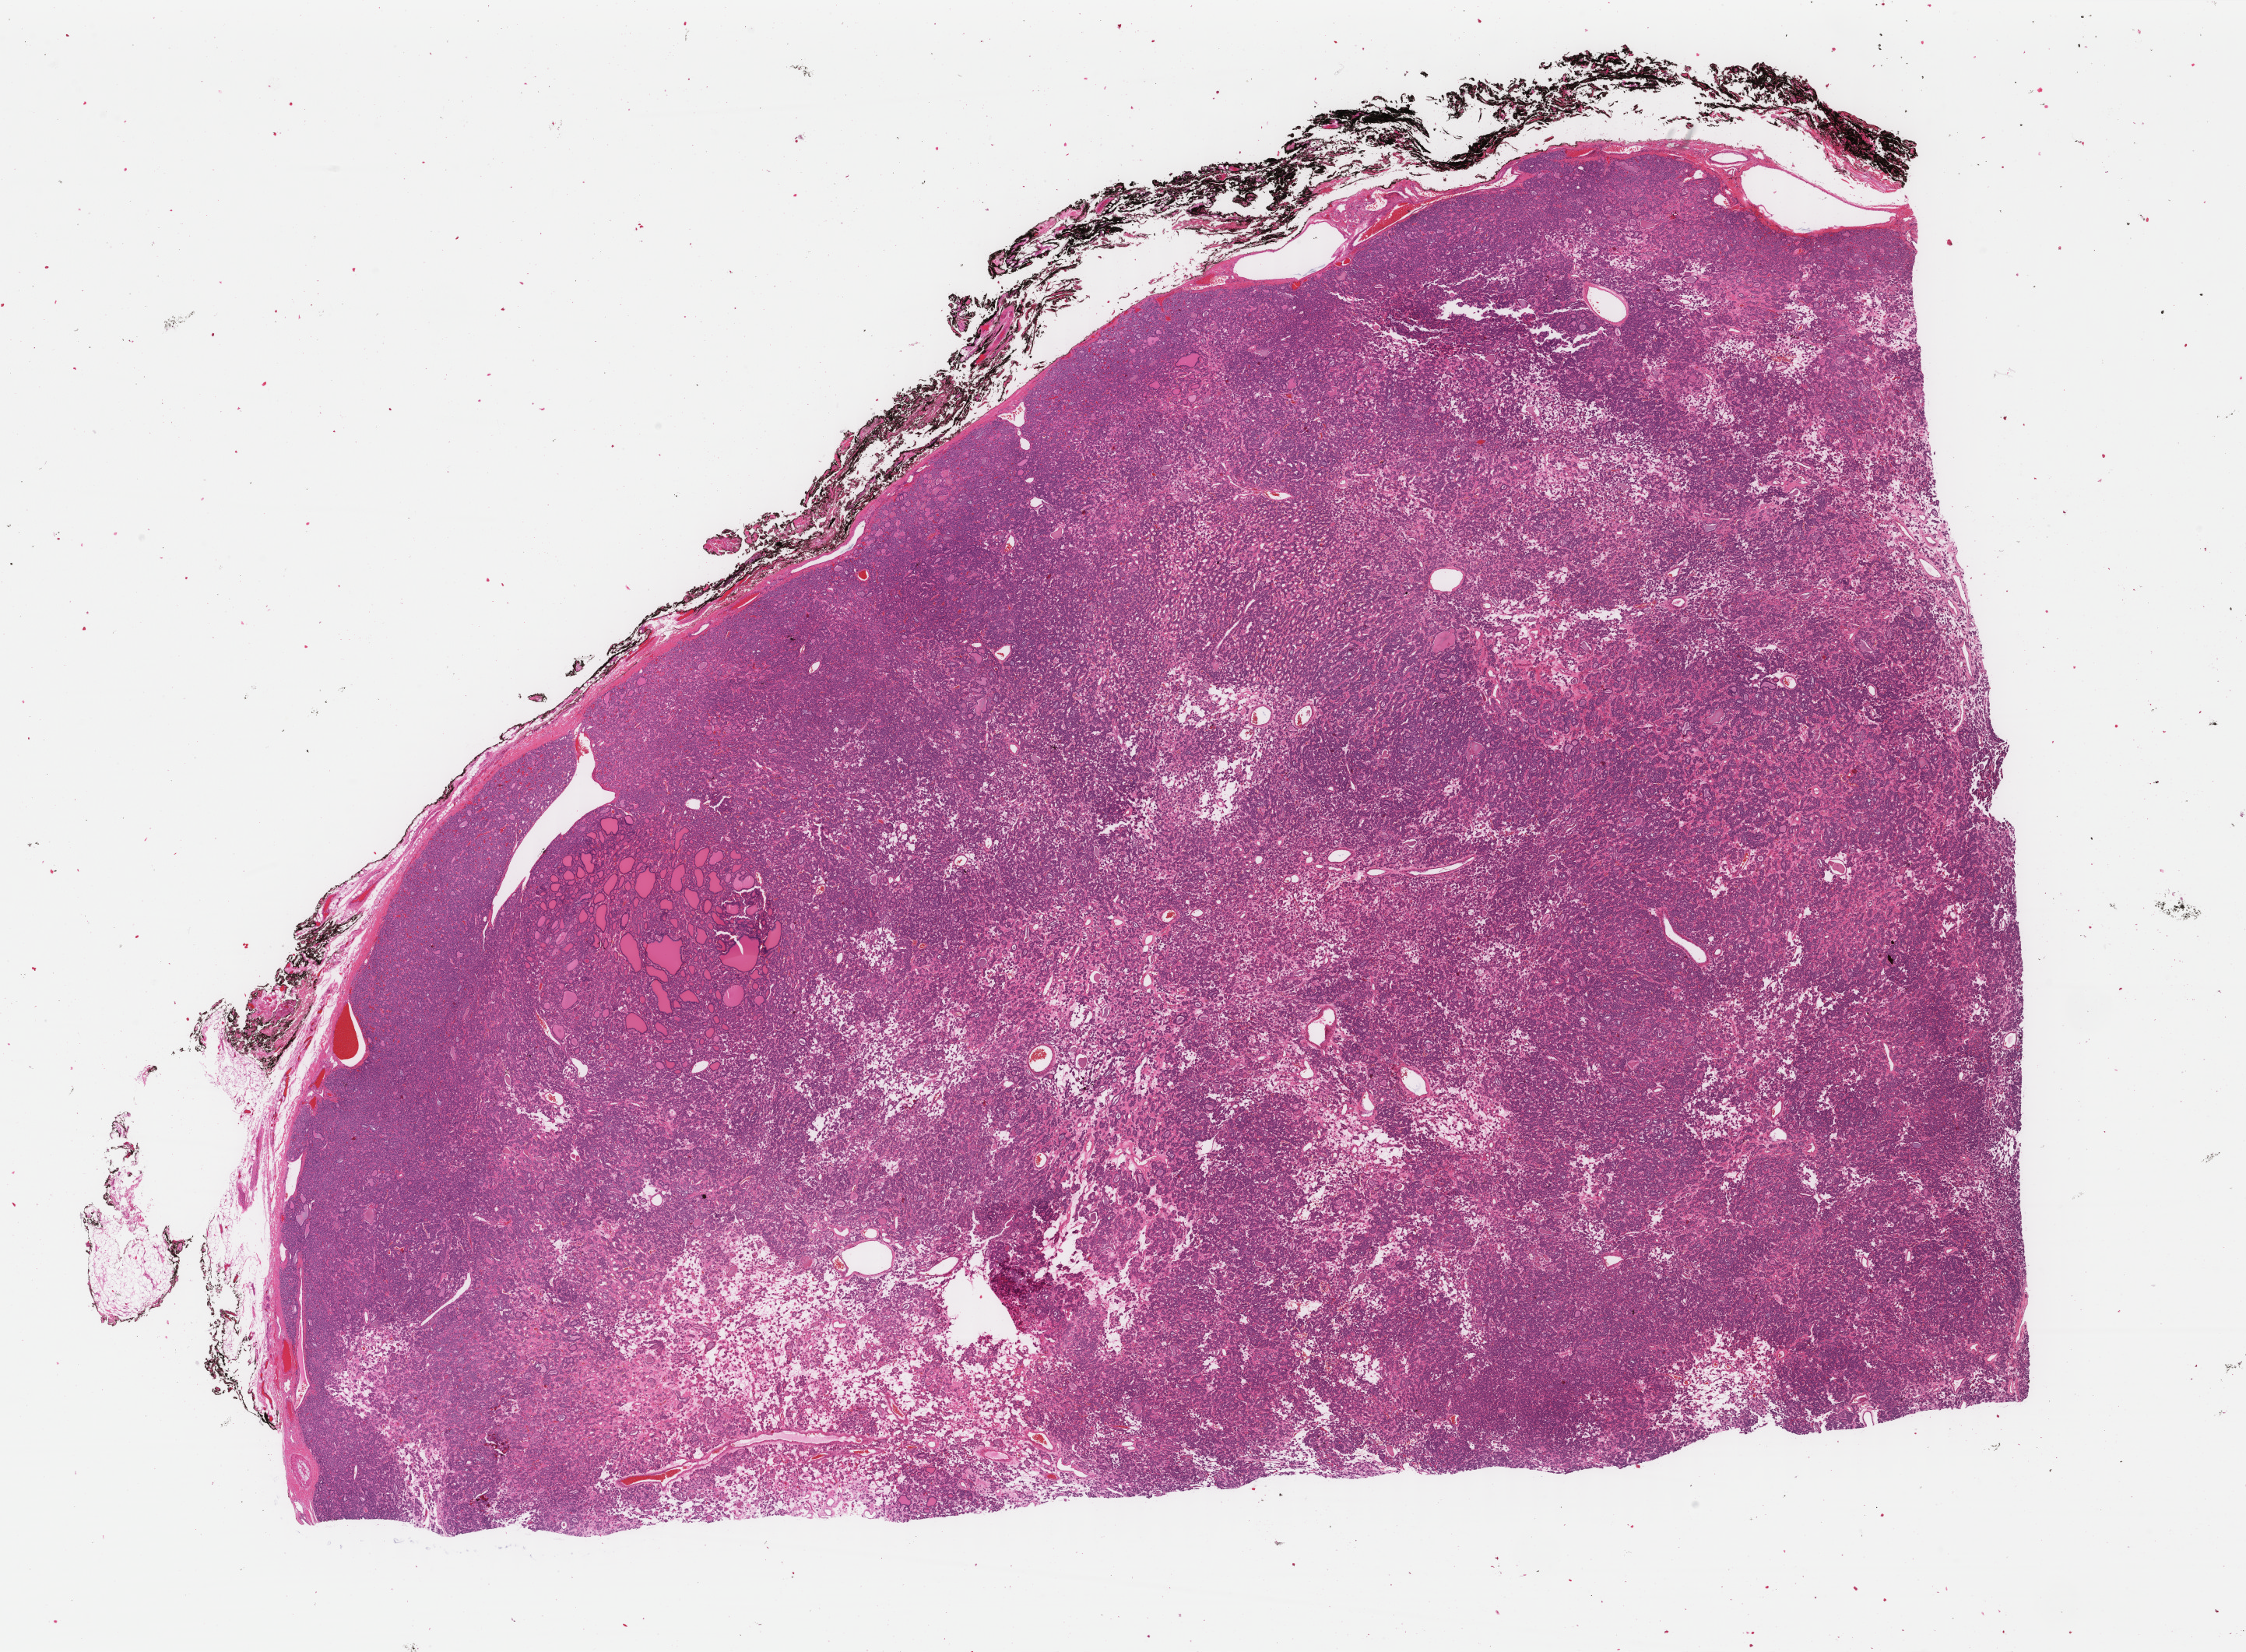
Whole-slide histology image, Hematoxylin and eosin (H&E) stained — whole scanned area (about 22.9 x 16.8 mm, slide scanned at 40x) shown as a low-resolution overview, FFPE section, primary tumour sample from the thyroid. Patient: female, age at initial diagnosis 68 years.
Pathologic diagnosis: Papillary carcinoma, follicular variant (thyroid gland).